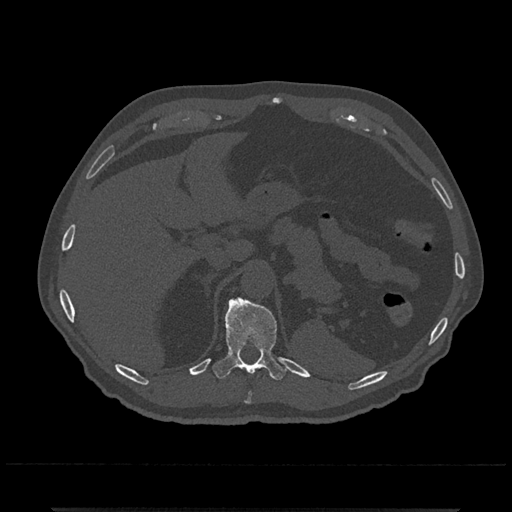
CT including the spine, one axial slice. Slice 500 of 797 in the series (ordered by position). 120 kVp. Bone window (W 1800 / L 400 HU). 512 × 512 image matrix, field of view 393 × 393 mm. Male patient, age 67 years. Case-level facts recorded for this patient, not image findings: primary cancer: prostate.
Structures marked on this image (semi-automatic segmentation, software-assisted and operator-edited):
- T10 vertebra: bounding box (x1, y1, x2, y2) in pixels: (246, 391, 252, 403)
- T11 vertebra: (212, 296, 287, 381)